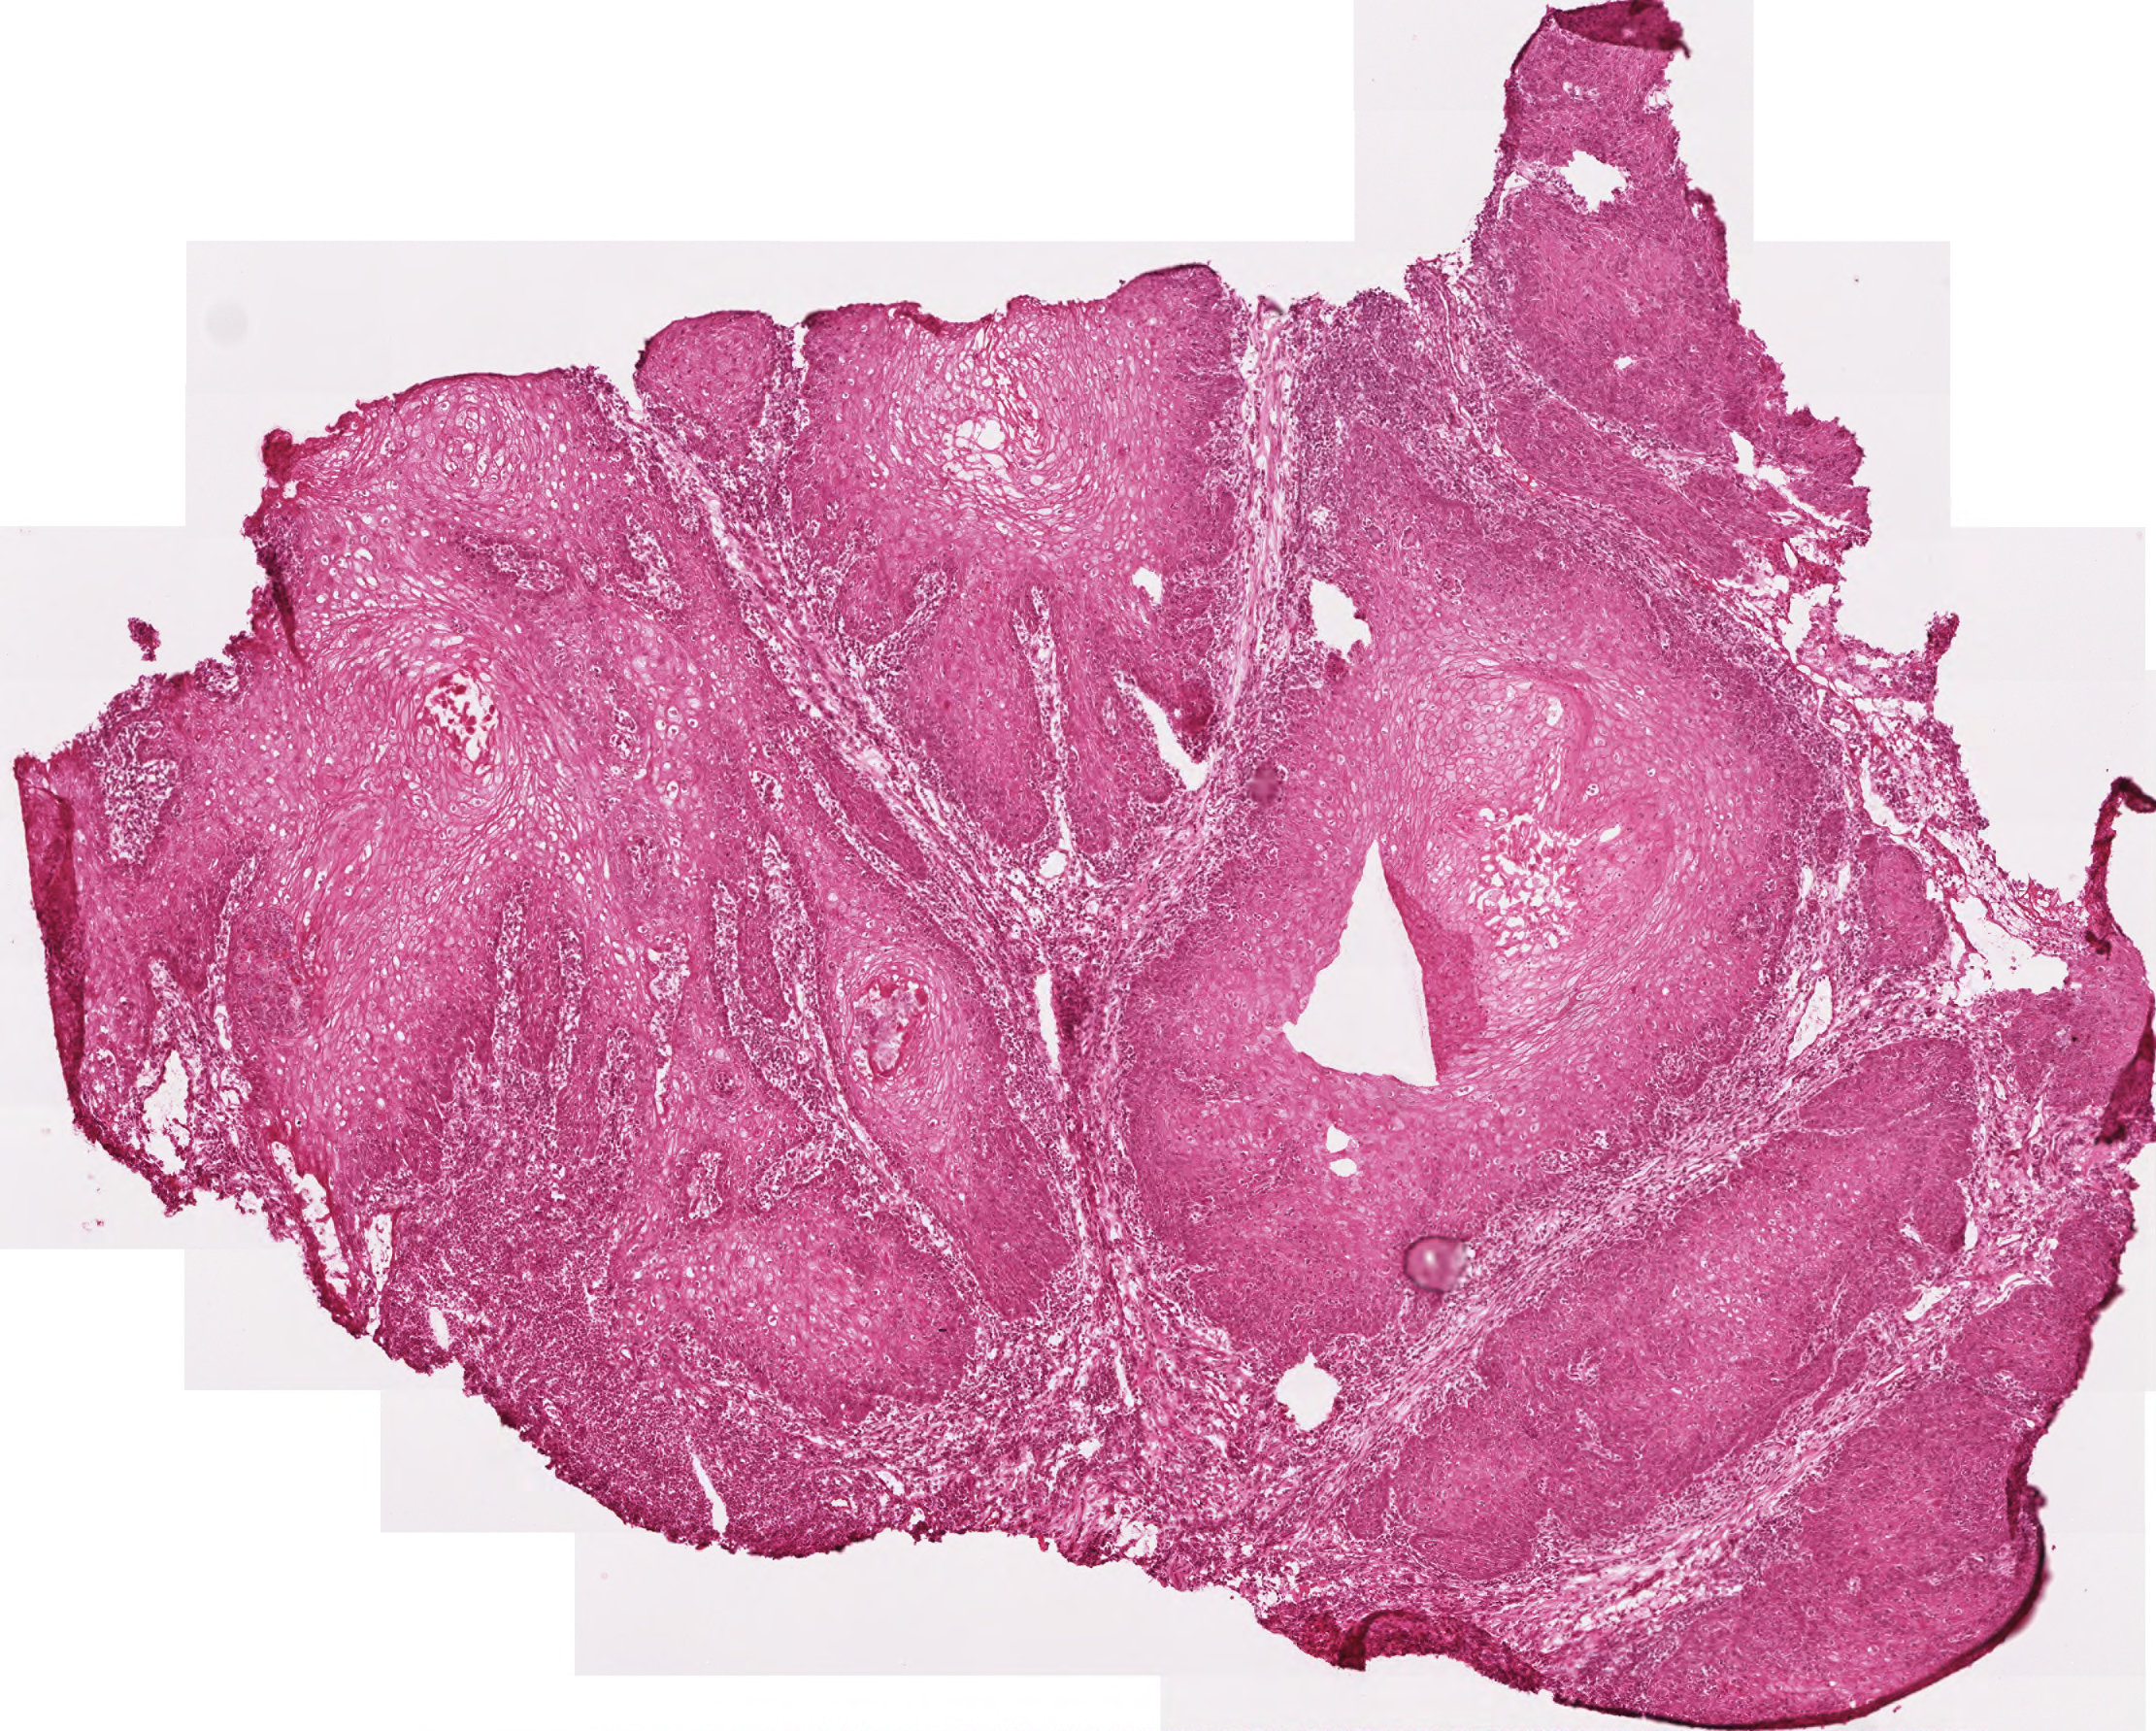
Digitized H&E-stained tissue section (whole slide), a low-resolution overview of the entire scanned area, about 2.2 x 1.8 mm; frozen section from the top of the tissue portion; sample: primary tumour, head and neck. Female patient; age at initial diagnosis 80 years. Histologic grade: G2 (moderately differentiated). Slide review estimates, as recorded: tumour cells 100%, tumour nuclei 61%, normal cells 0%, stromal cells 0%, necrosis 0%. Infiltration values recorded for this section: lymphocyte infiltration 35%, monocyte infiltration 0%, neutrophil infiltration 0%.
* AJCC pathologic stage: II
* histologic diagnosis: Squamous cell carcinoma, NOS (overlapping lesion of lip, oral cavity and pharynx)